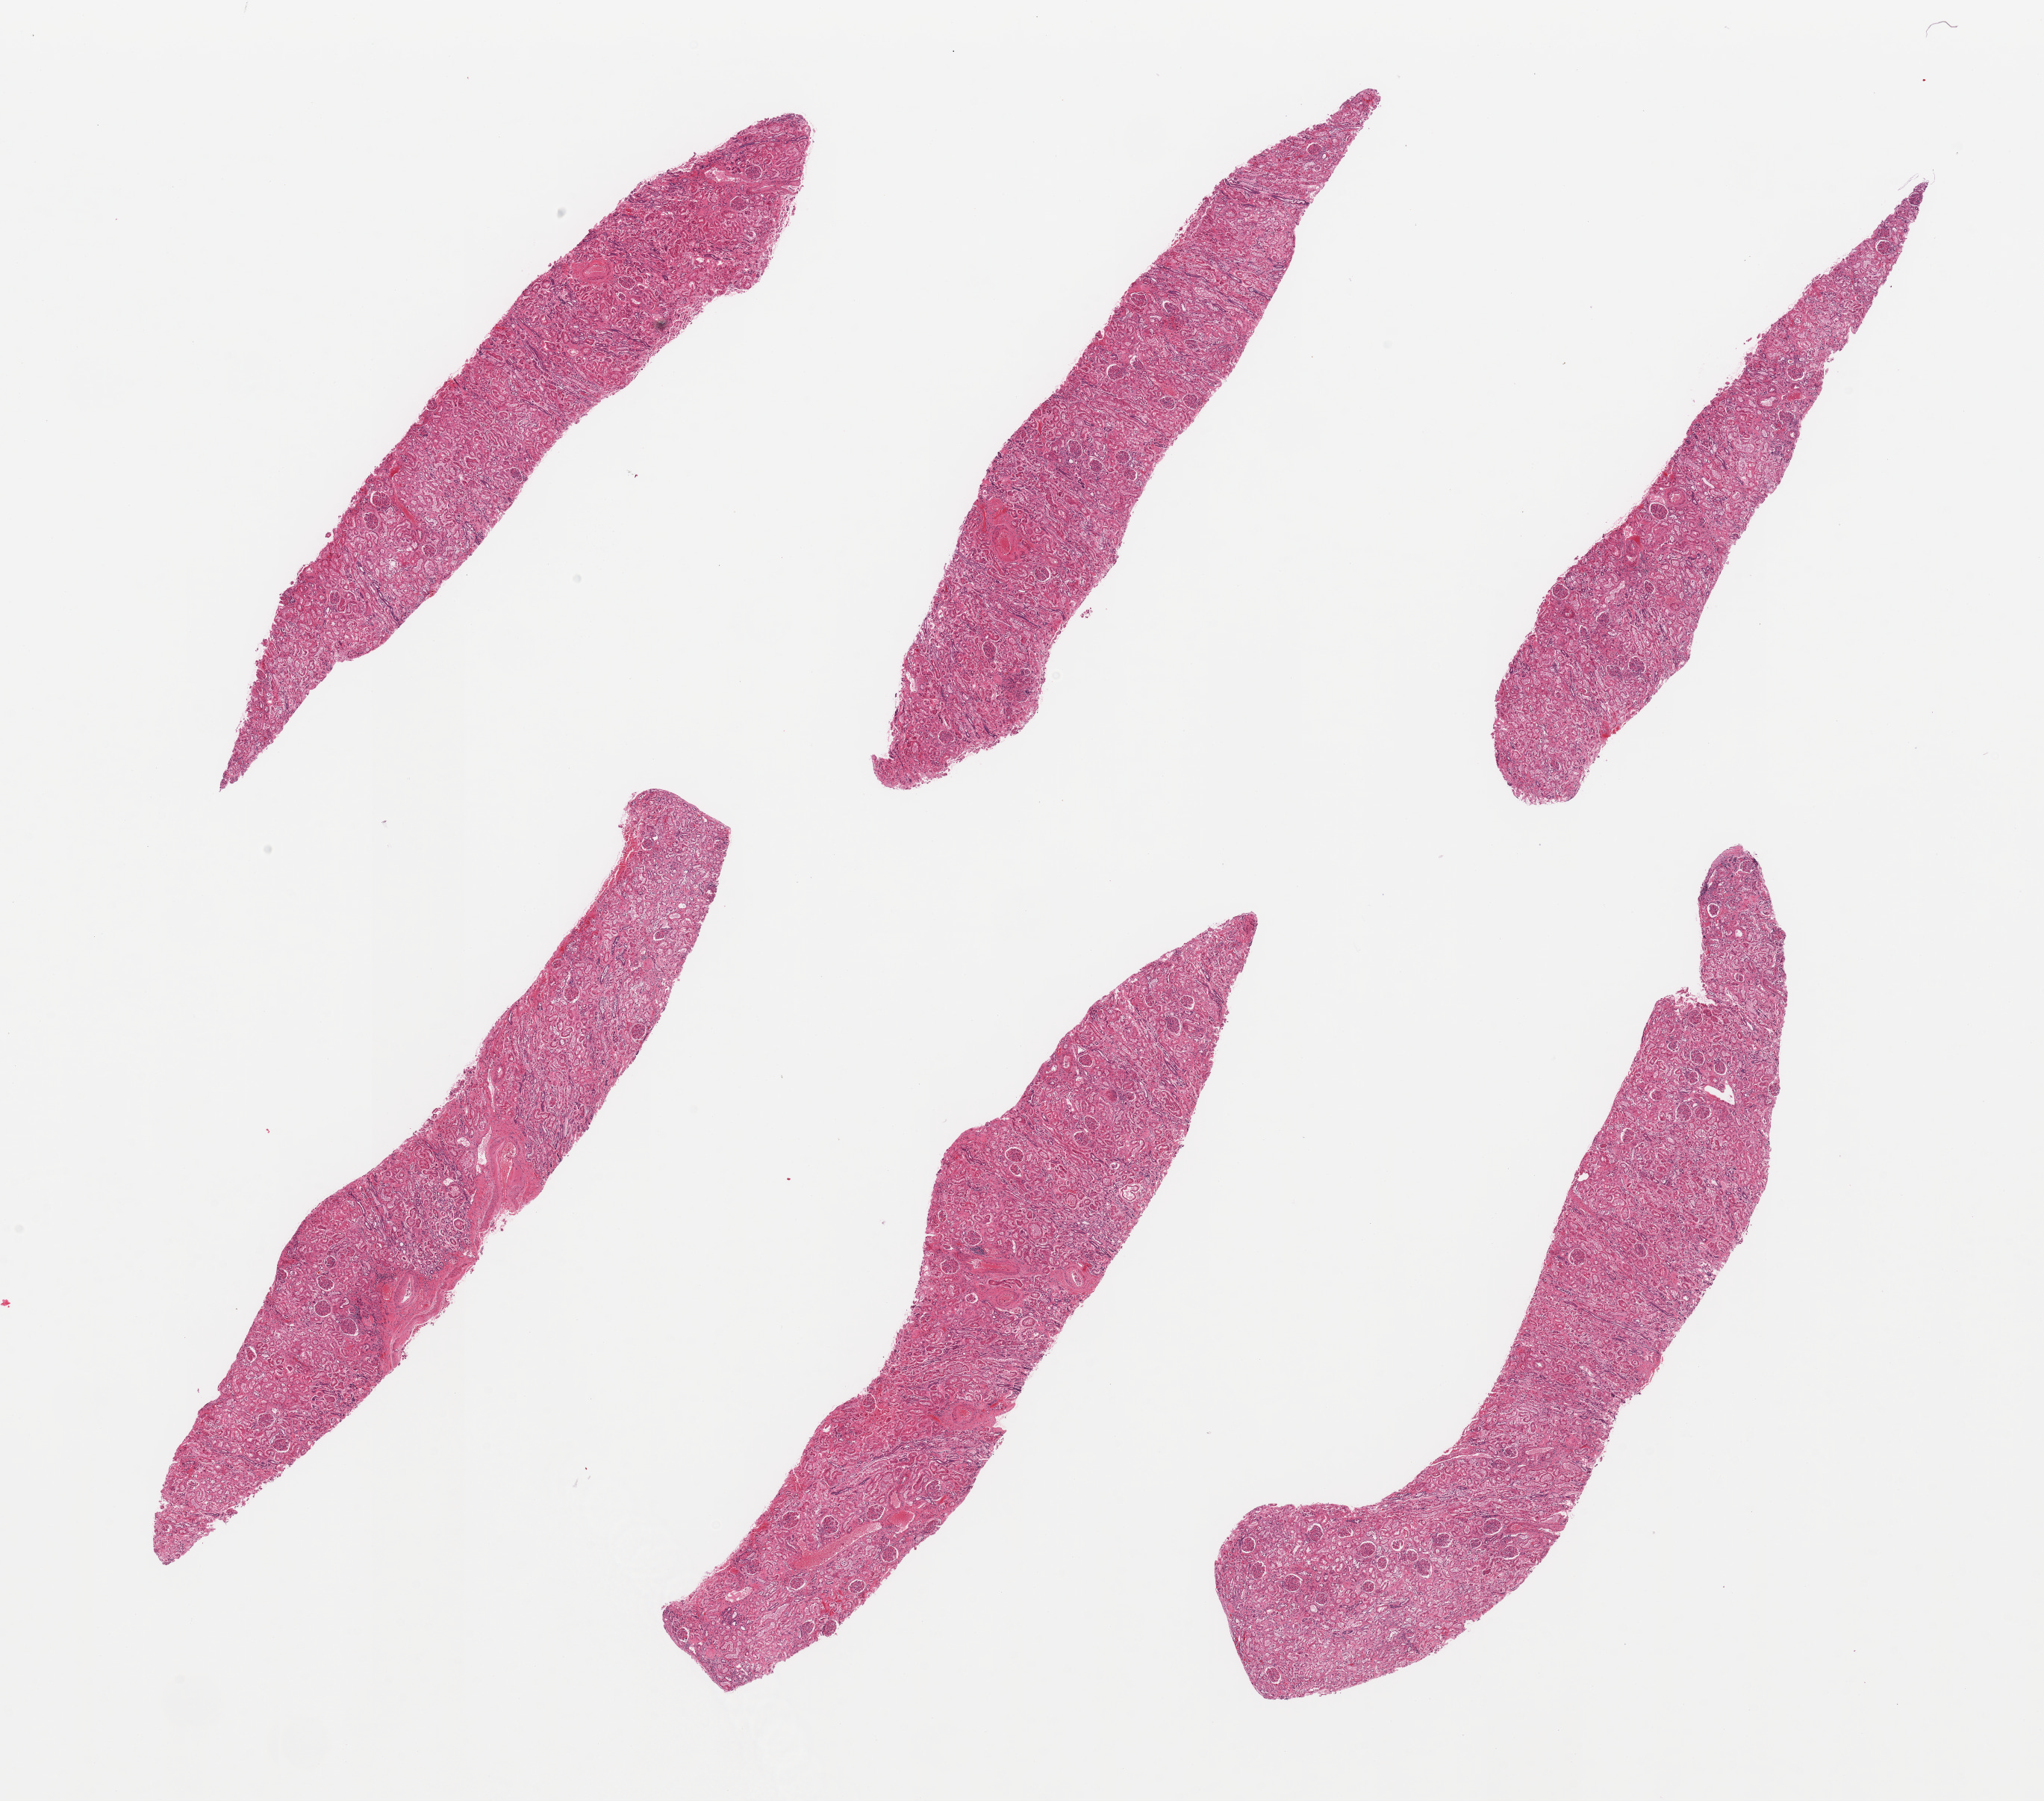
Digitized H&E-stained section — shown as a low-resolution overview of the whole scanned area (about 21.7 x 19.1 mm), PAXgene-fixed, paraffin-embedded tissue, target tissue: renal cortex, tissue donor sample.
Review note (as recorded): 6 pieces, glomeruli present; moderate tubular autolysis.